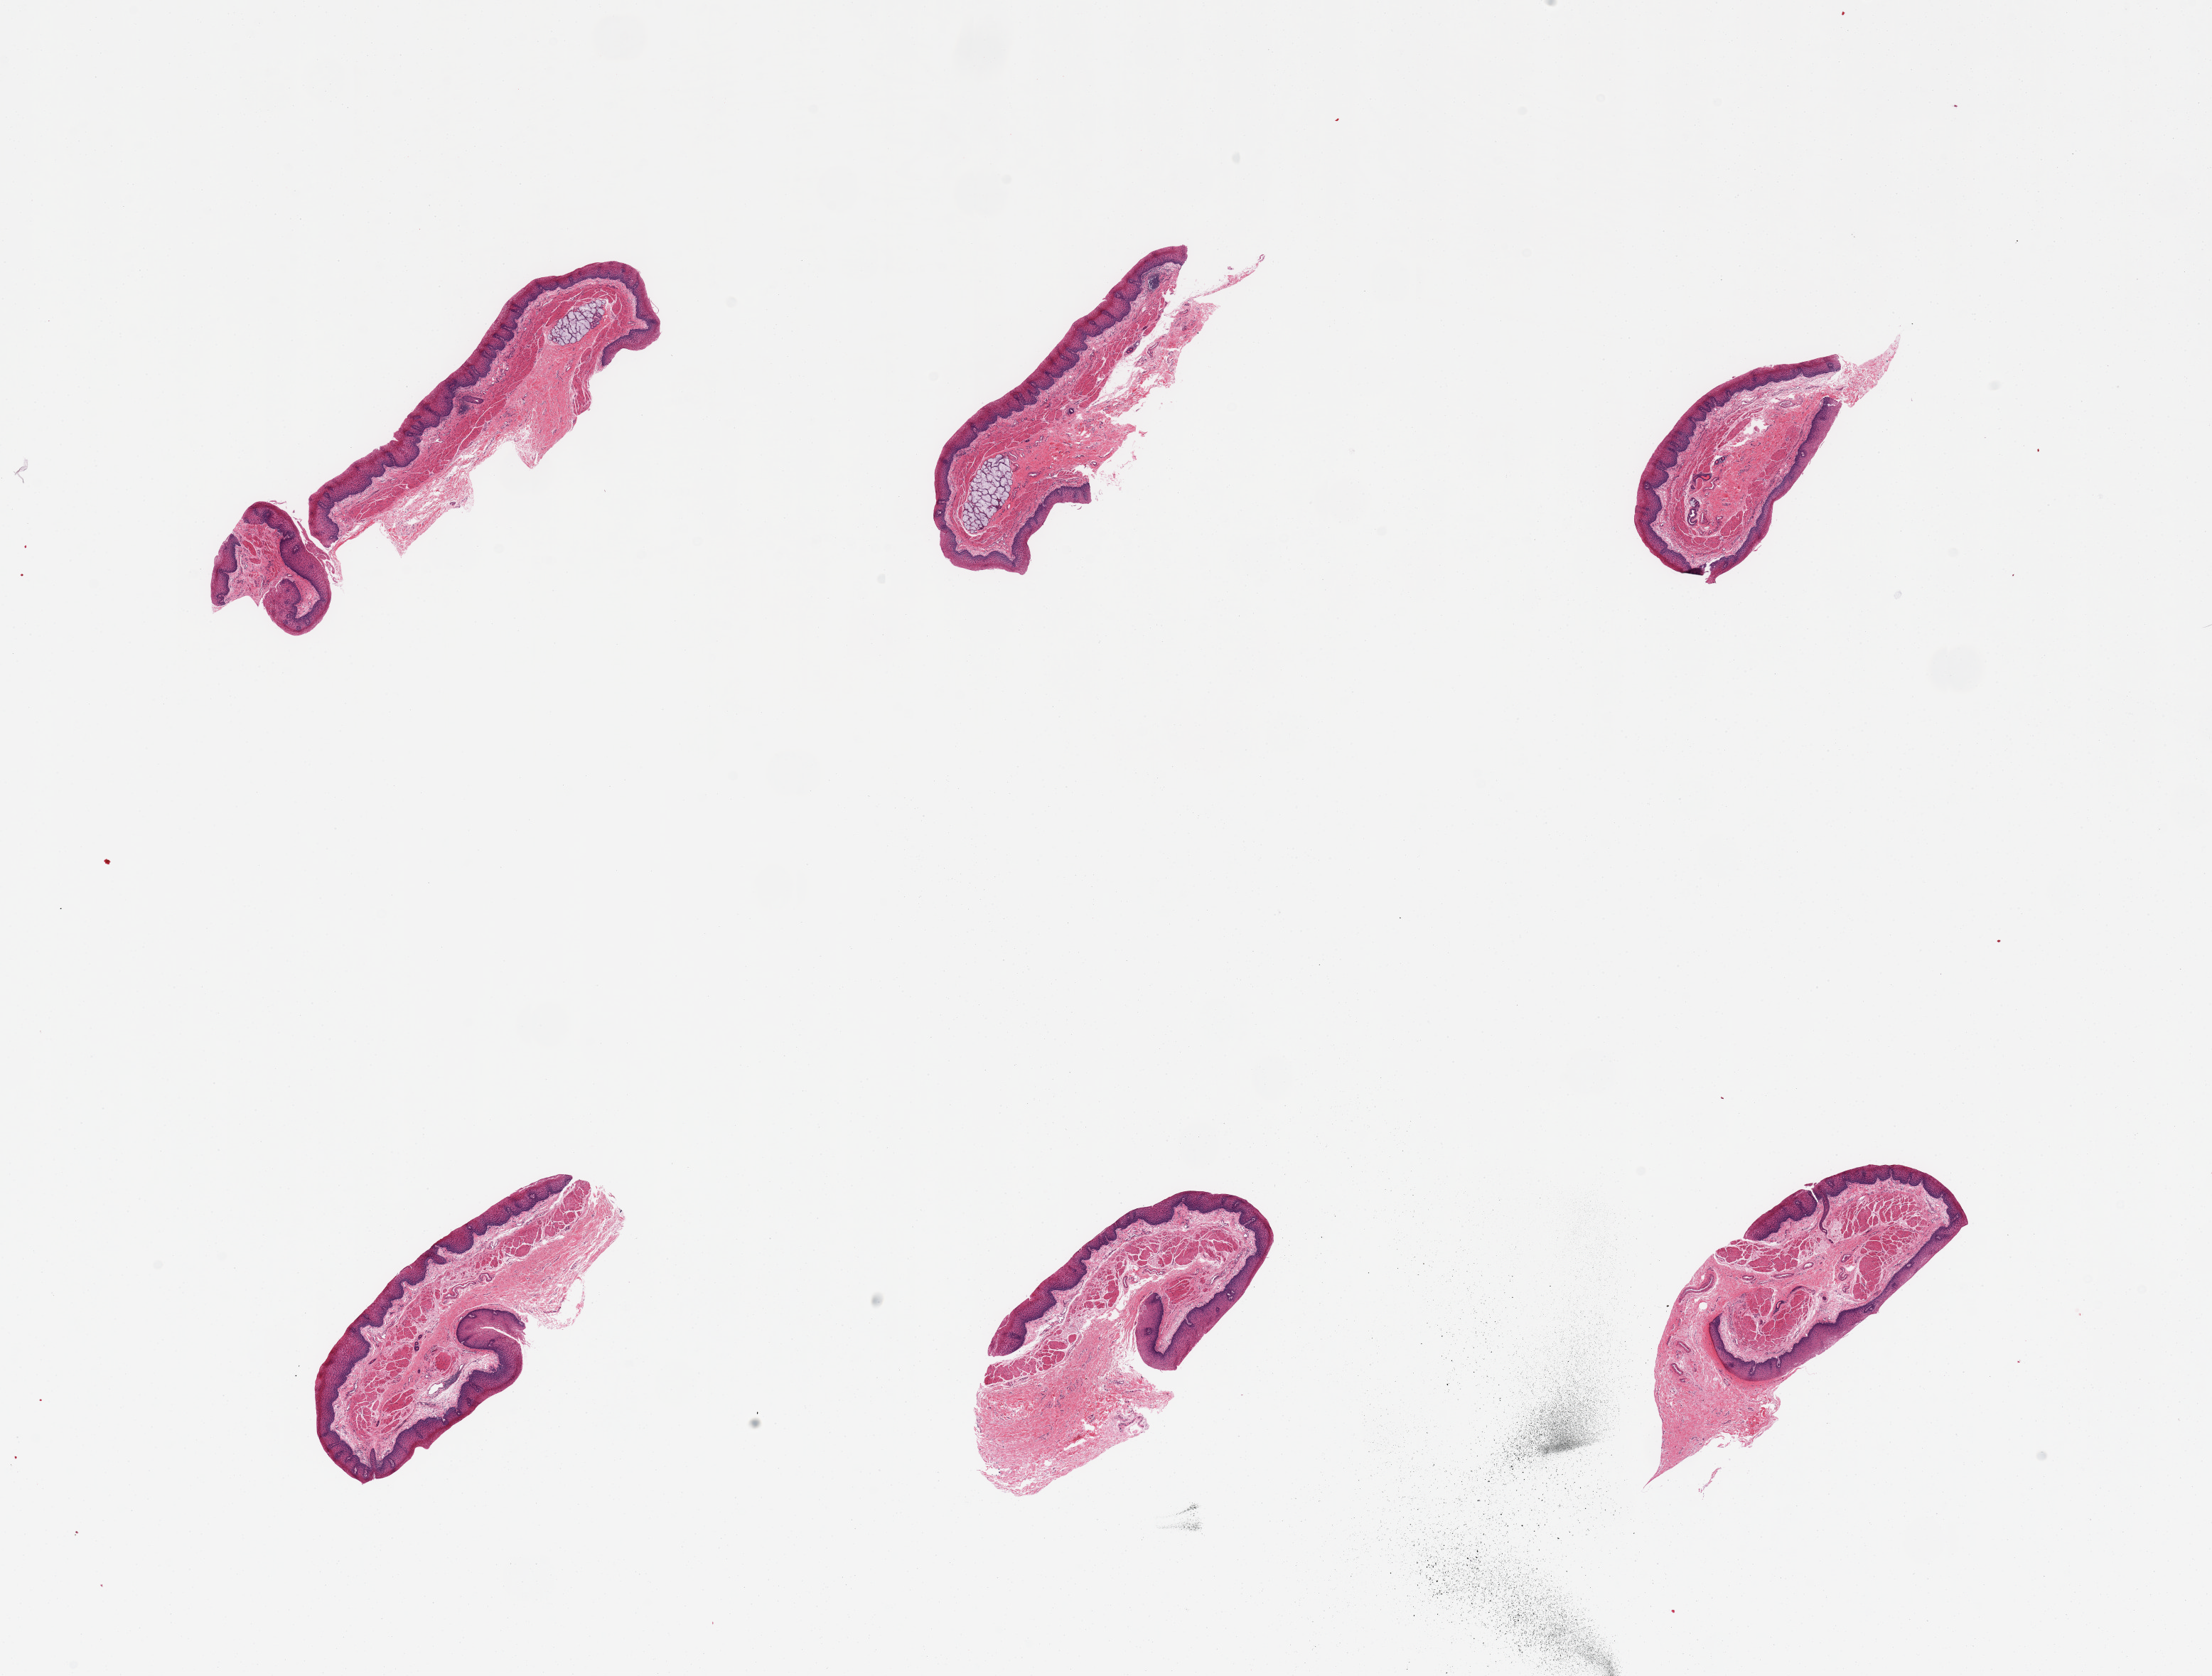
H&E whole-slide image, low-resolution overview of the scanned area, about 24.6 x 18.6 mm, PAXgene-fixed paraffin-embedded (PFPE) section, target tissue: esophageal mucous membrane, tissue donor sample. Donor: female.
Pathologist's review note for this sample: 6 pieces; prominent submucosal glands (1 mm).